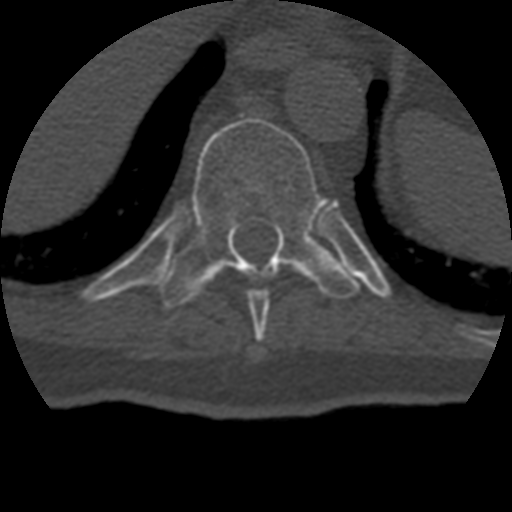
CT including the spine, one axial slice. Slice 225 of 399 in the series (ordered by position). Reconstruction kernel STANDARD. 120 kVp. Bone window (W 1800 / L 400 HU). 512 × 512 image matrix, field of view 160 × 160 mm. Patient age 69 years. Case-level facts recorded for this patient, not image findings: primary cancer: prostate.
Annotated regions visible in this slice (semi-automatically segmented with operator editing):
- T10 vertebra: bounding box (x1, y1, x2, y2) in pixels: (160, 118, 360, 308)
- T9 vertebra: (247, 290, 270, 335)